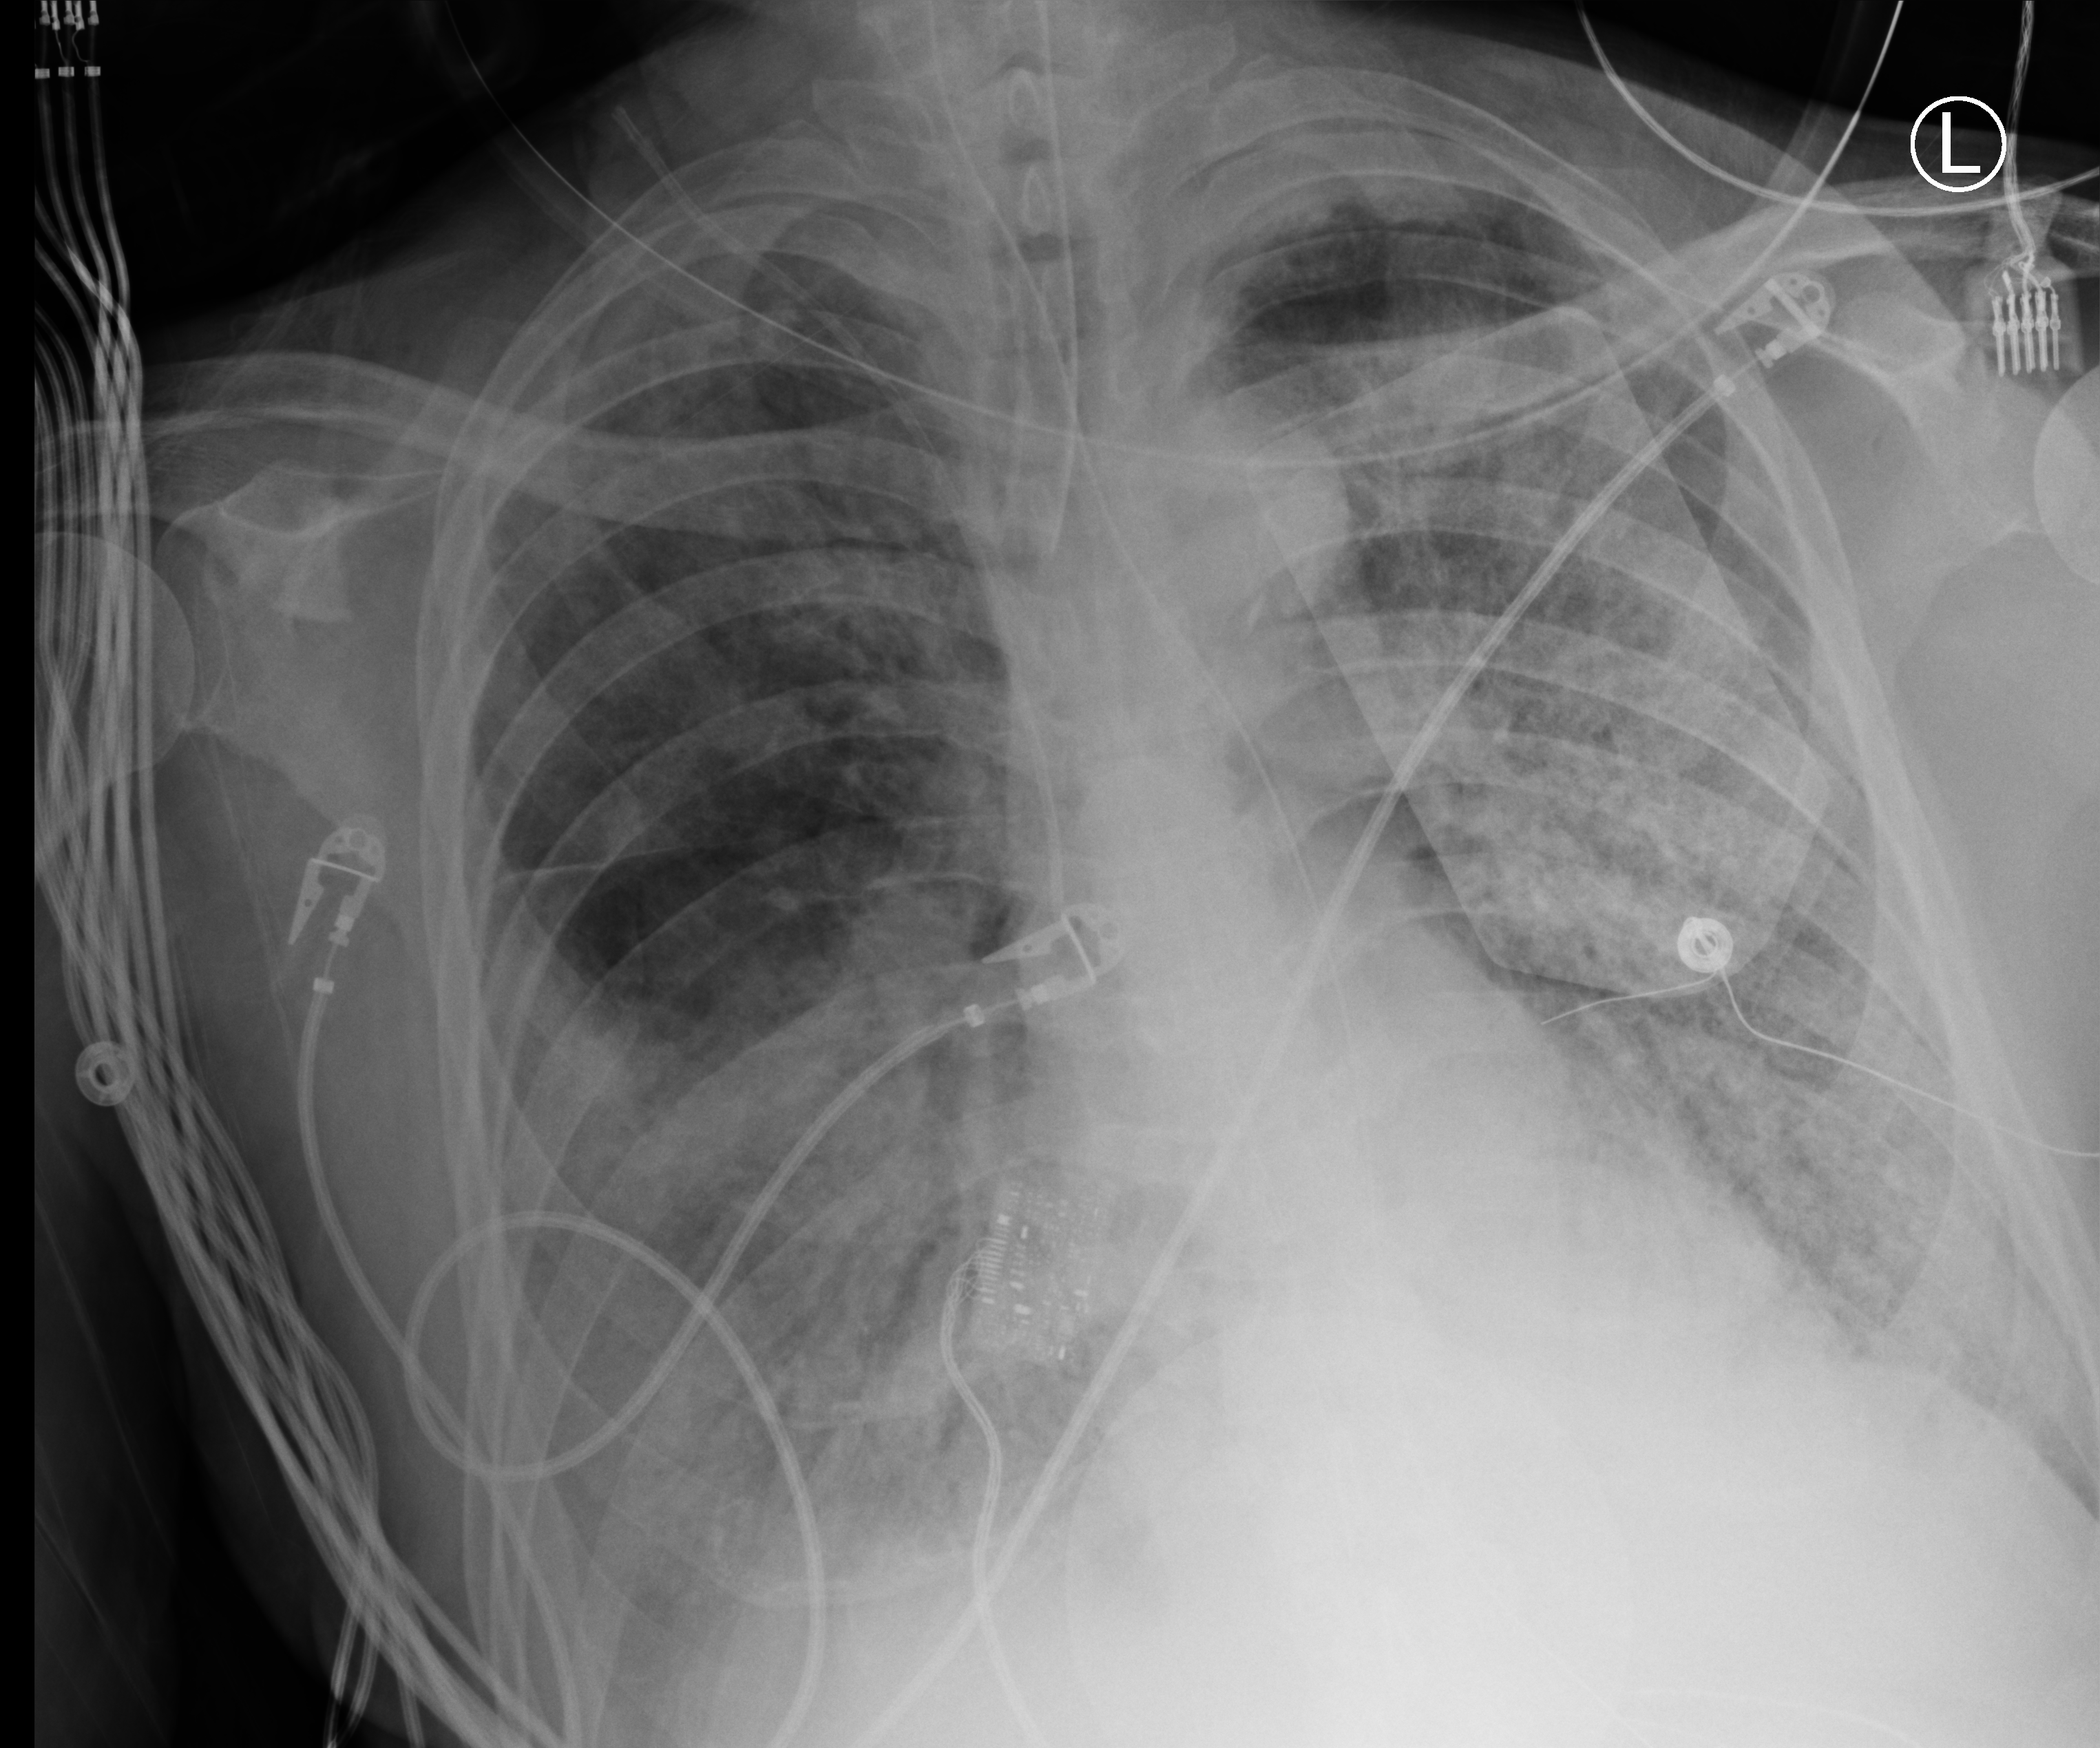
Portable chest radiograph; anteroposterior (AP) projection. Patient hospitalised with COVID-19; male, aged 60–74 years.
Admission-level facts for this patient (not findings on this image; timing relative to this image not recorded): length of hospital stay: 31 days; admitted to intensive care during this hospital stay: yes.